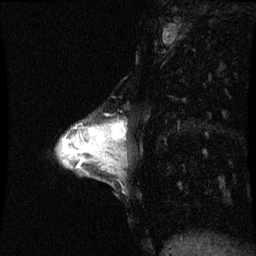
Breast MRI (dynamic contrast-enhanced), one sagittal slice; position 25 of 60 along the scan axis; dynamic contrast-enhanced series, image 2 of 3 at this slice position (ordered by acquisition); 1.5 T; TE 4.2 ms, TR 8.9 ms; 2 mm slice thickness; 256 × 256 image matrix, field of view 200 × 200 mm. Patient: female, 33 years. From the clinical record (not read from this slice): setting: breast cancer imaged before/during neoadjuvant chemotherapy; receptor status: HER2-positive.
Structures marked on this image (semi-automatically segmented with operator editing):
- analysis volume of interest (the breast-tissue region the enhancement analysis was run in; not a lesion): bounding box [x1, y1, x2, y2] px = [95, 124, 126, 153]
- tumour enhancement mask (voxels above the 70 % enhancement threshold inside the analysis volume of interest): [101, 124, 123, 141]